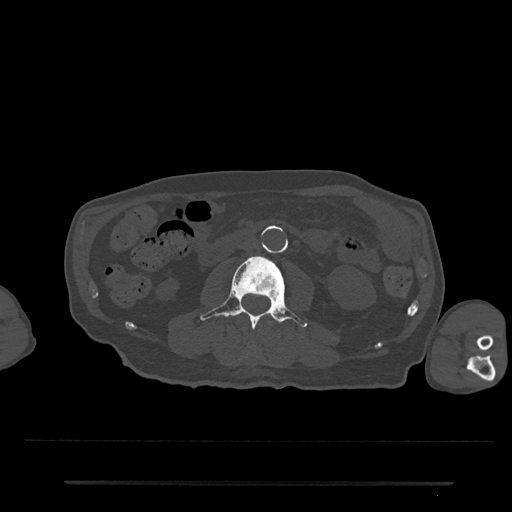
CT including the spine, one axial slice; position 1 of 797 along the scan axis; reconstruction kernel Br40s/3; bone window (W 1800 / L 400 HU); 0.5 mm slice thickness; 512 × 512 image matrix, field of view 427 × 427 mm. Male patient, age 74 years. Case-level facts recorded for this patient, not image findings: primary cancer: prostate.
Annotated regions visible in this slice (semi-automatic segmentation, software-assisted and operator-edited):
- L2 vertebra: bounding box [x1, y1, x2, y2] px = [246, 316, 275, 358]
- L3 vertebra: [200, 256, 308, 328]